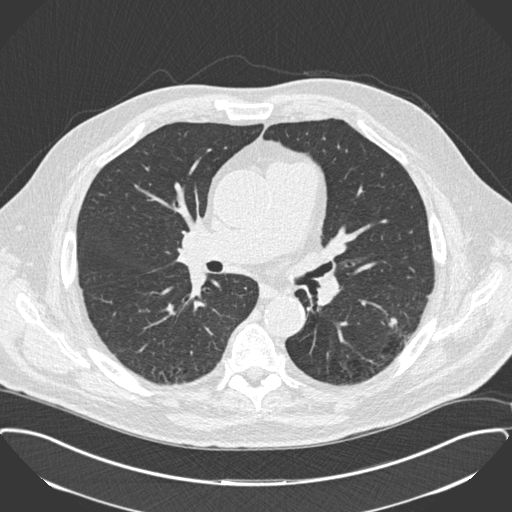
Low-dose screening chest CT, one axial slice; position 98 of 175 along the scan axis; 120 kVp; lung window (W 1500 / L -600 HU); 2 mm slice thickness; 512 × 512 image matrix, field of view 400 × 400 mm.
Annotated regions visible in this slice (expert manual segmentation):
- lesion 1 (tumor, lower lobe of left lung): bounding box <389,318,397,327> (left, top, right, bottom; pixels)